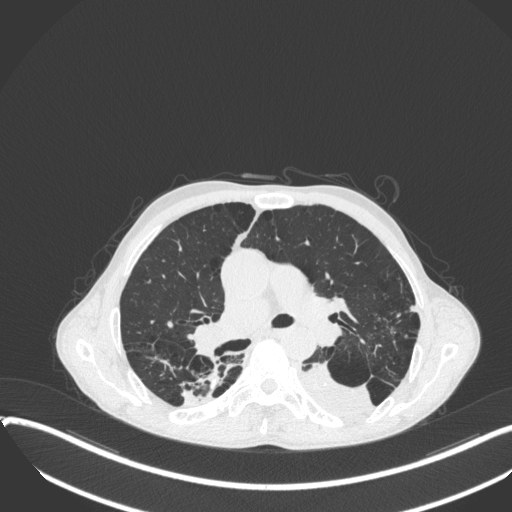
Chest CT, one axial slice; slice 233 of 400 in the series (ordered by position); reconstruction kernel B31f; lung window (W 1500 / L -600 HU); 512 × 512 image matrix, field of view 400 × 400 mm. Patient: male, 57 years. Case-level facts recorded for this patient, not image findings: clinical TNM (as recorded): T4 N0 M0.
Annotated regions visible in this slice (bounding box drawn by a radiologist):
- lung tumour (recorded histology: squamous cell carcinoma): bounding box [x1, y1, x2, y2] px = [297, 359, 376, 418]